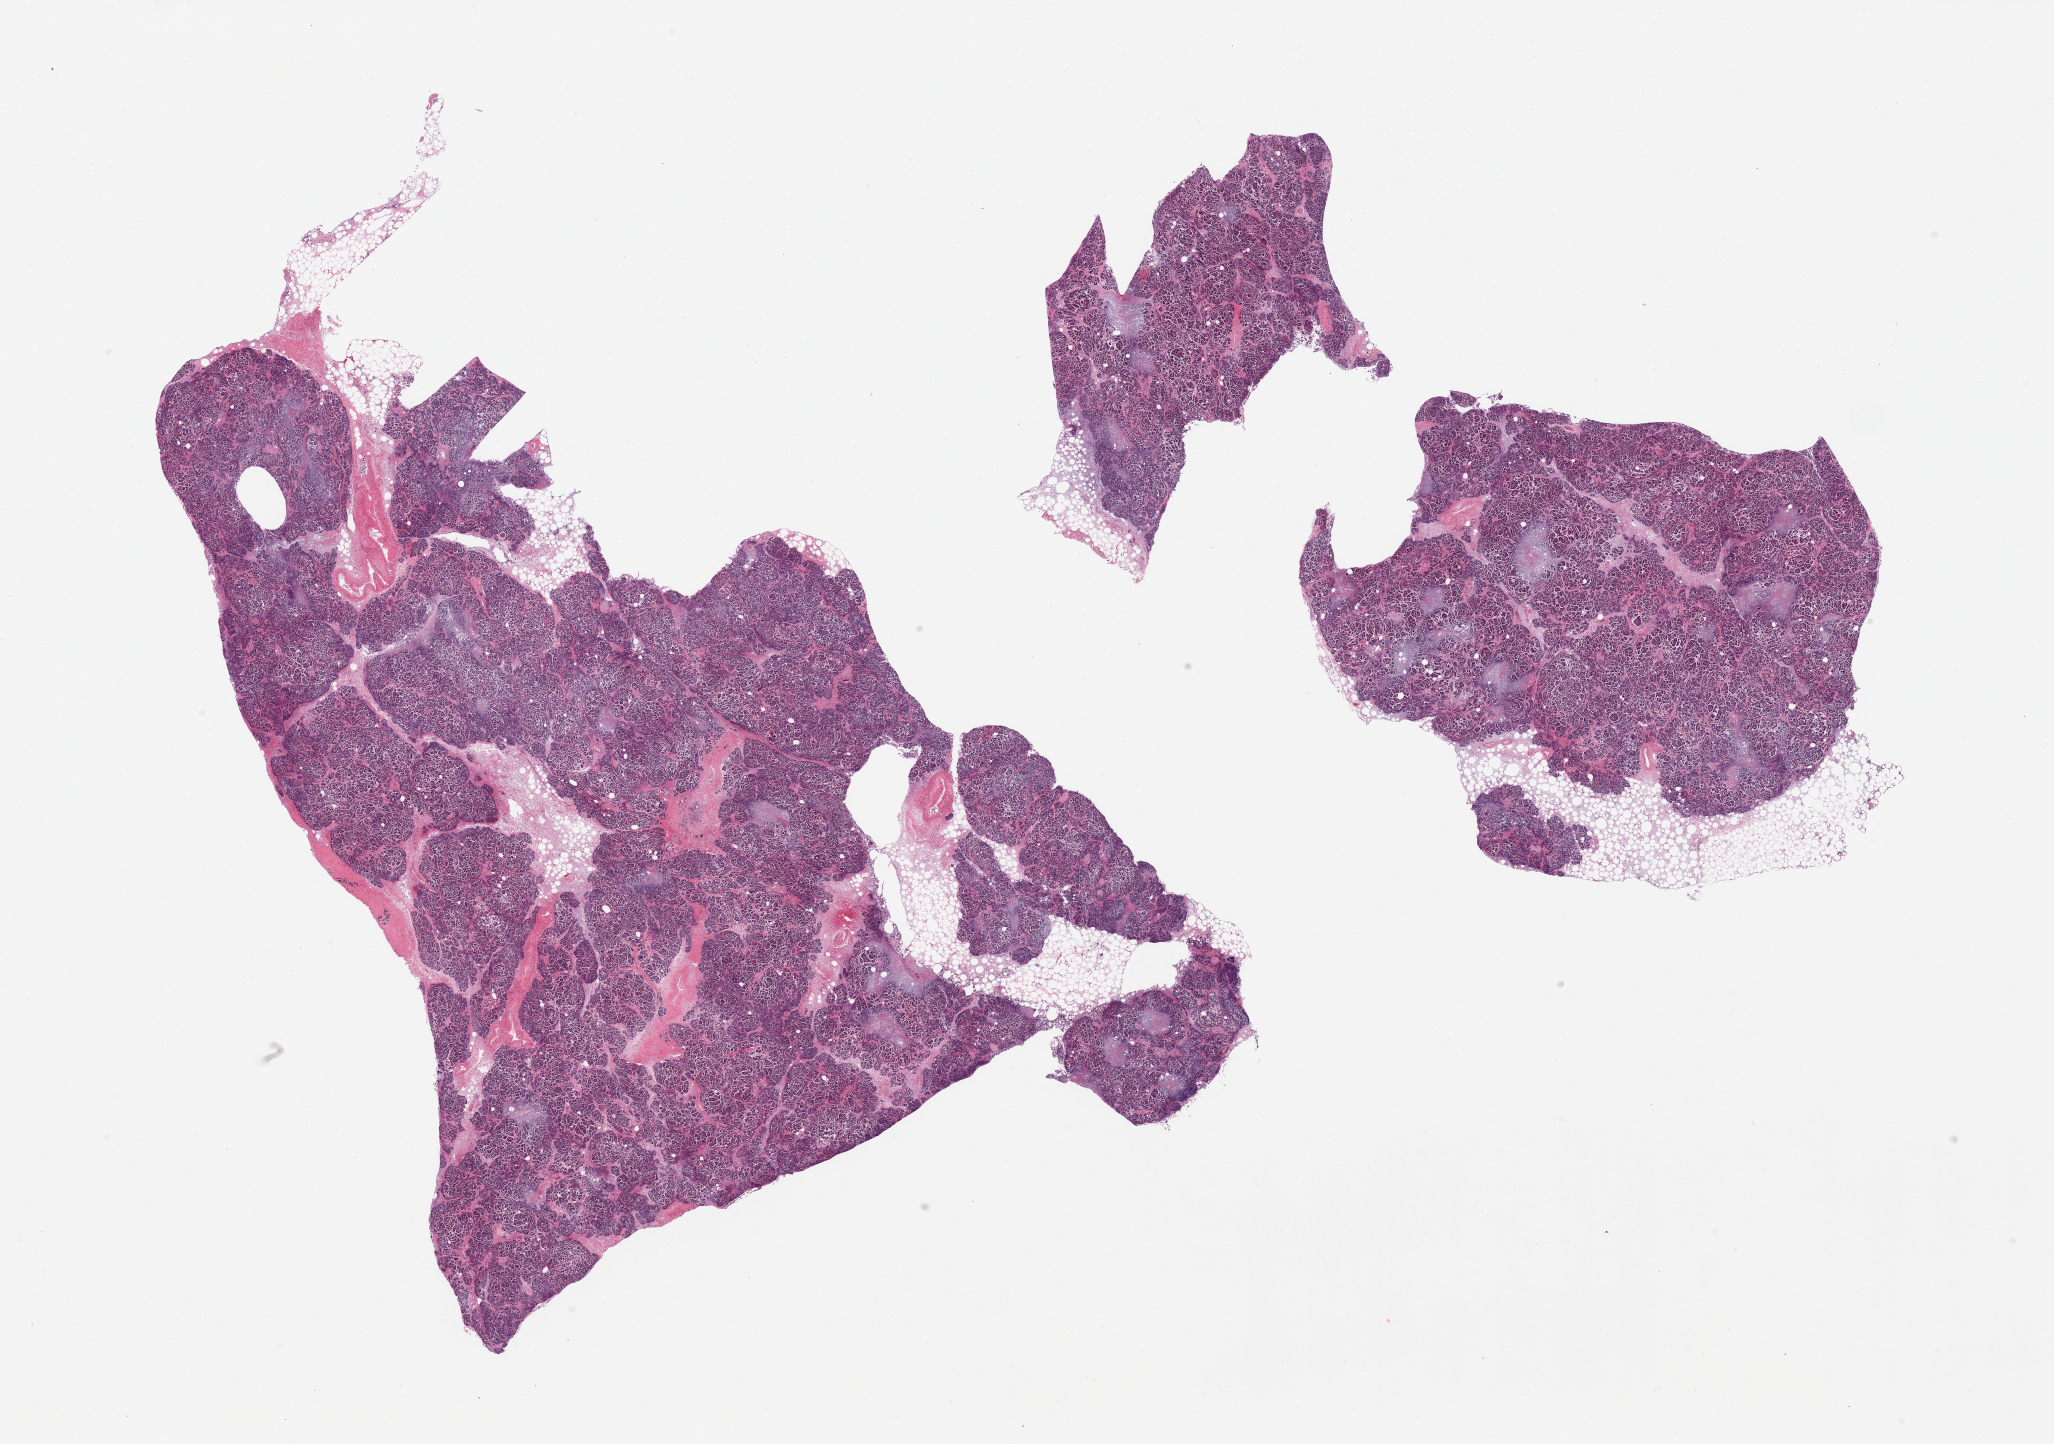
Hematoxylin and eosin (H&E) whole-slide image, brightfield — low-resolution overview of the scanned area, about 32.5 x 22.8 mm (acquisition: 20x scan); PAXgene-fixed, paraffin-embedded tissue; section of pancreas (target tissue); tissue donor sample. Donor: male.
• pathologist's review note for this sample: 2 pieces, saponification/autolysis preclude identification of Islets